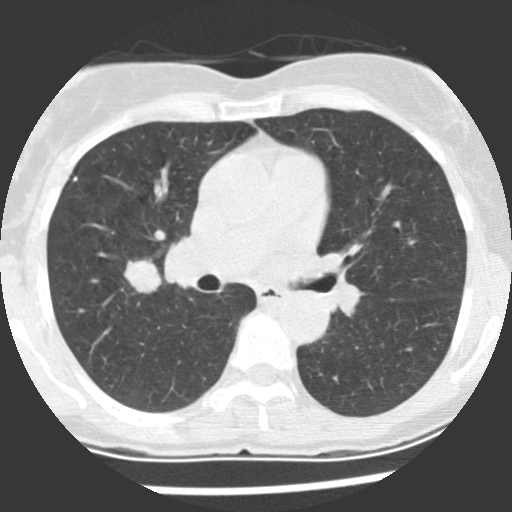
Chest CT (low-dose screening protocol), one axial image, baseline screening round, lung window (W 1500 / L -600 HU), 2.5 mm slice thickness, slice 101 of 225 in the series, 512 × 512 image matrix. Female participant, aged 60 years at enrolment.
Lesion marked by an expert reader, bounding box (x1, y1, x2, y2) in pixels: (115, 255, 172, 301). The screening reader recorded 2 non-calcified nodules or masses ≥4 mm on this exam (right upper lobe, right middle lobe); which of them this box marks is not recorded. Official screen result: positive, change unspecified: nodule(s) >= 4 mm or enlarging nodule(s), mass(es), or other non-specific abnormalities suspicious for lung cancer. Lung cancer was diagnosed 10 days after this screen: adenocarcinoma, NOS, right upper lobe, stage IIIA (AJCC 6th edition), 20 mm at pathology.